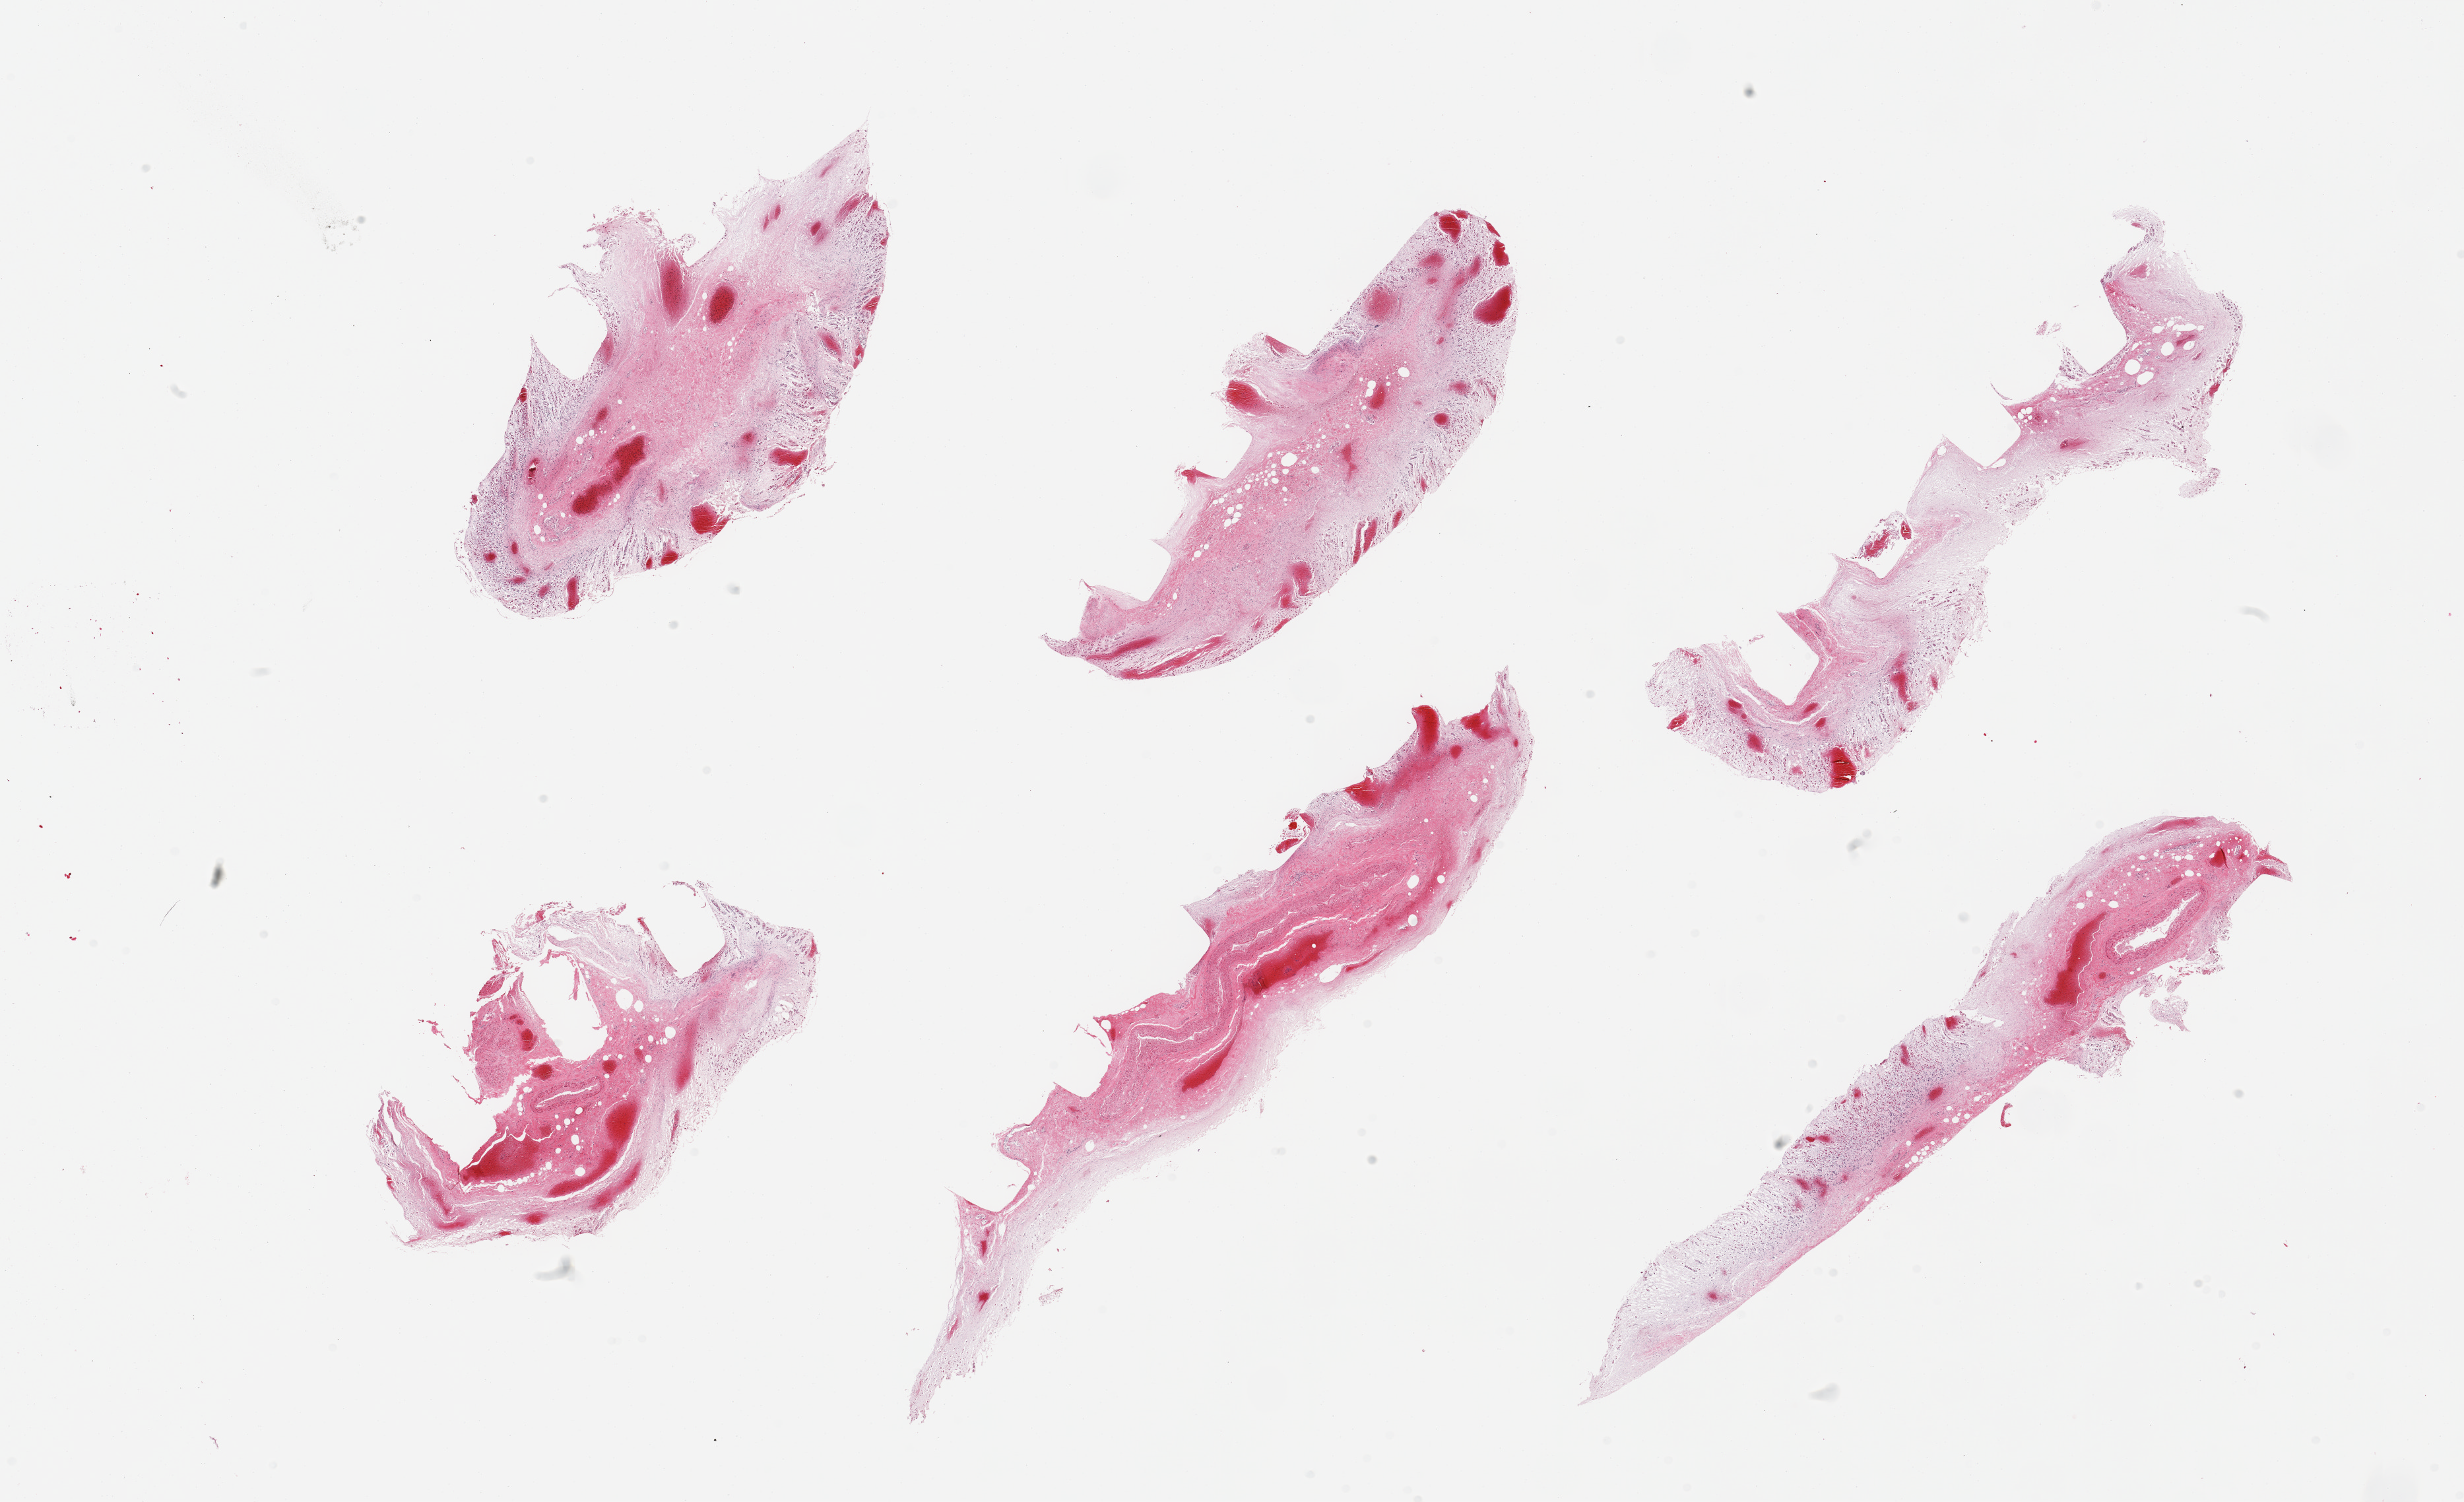
Digitized hematoxylin and eosin (H&E)-stained section, shown as a low-resolution overview of the whole scanned area (about 29.5 x 18.0 mm); PAXgene-fixed, paraffin-embedded tissue; target tissue: stomach; donor tissue sample. Male donor.
Reviewer comment on this tissue sample: 6 pieces; totally autolyzed.